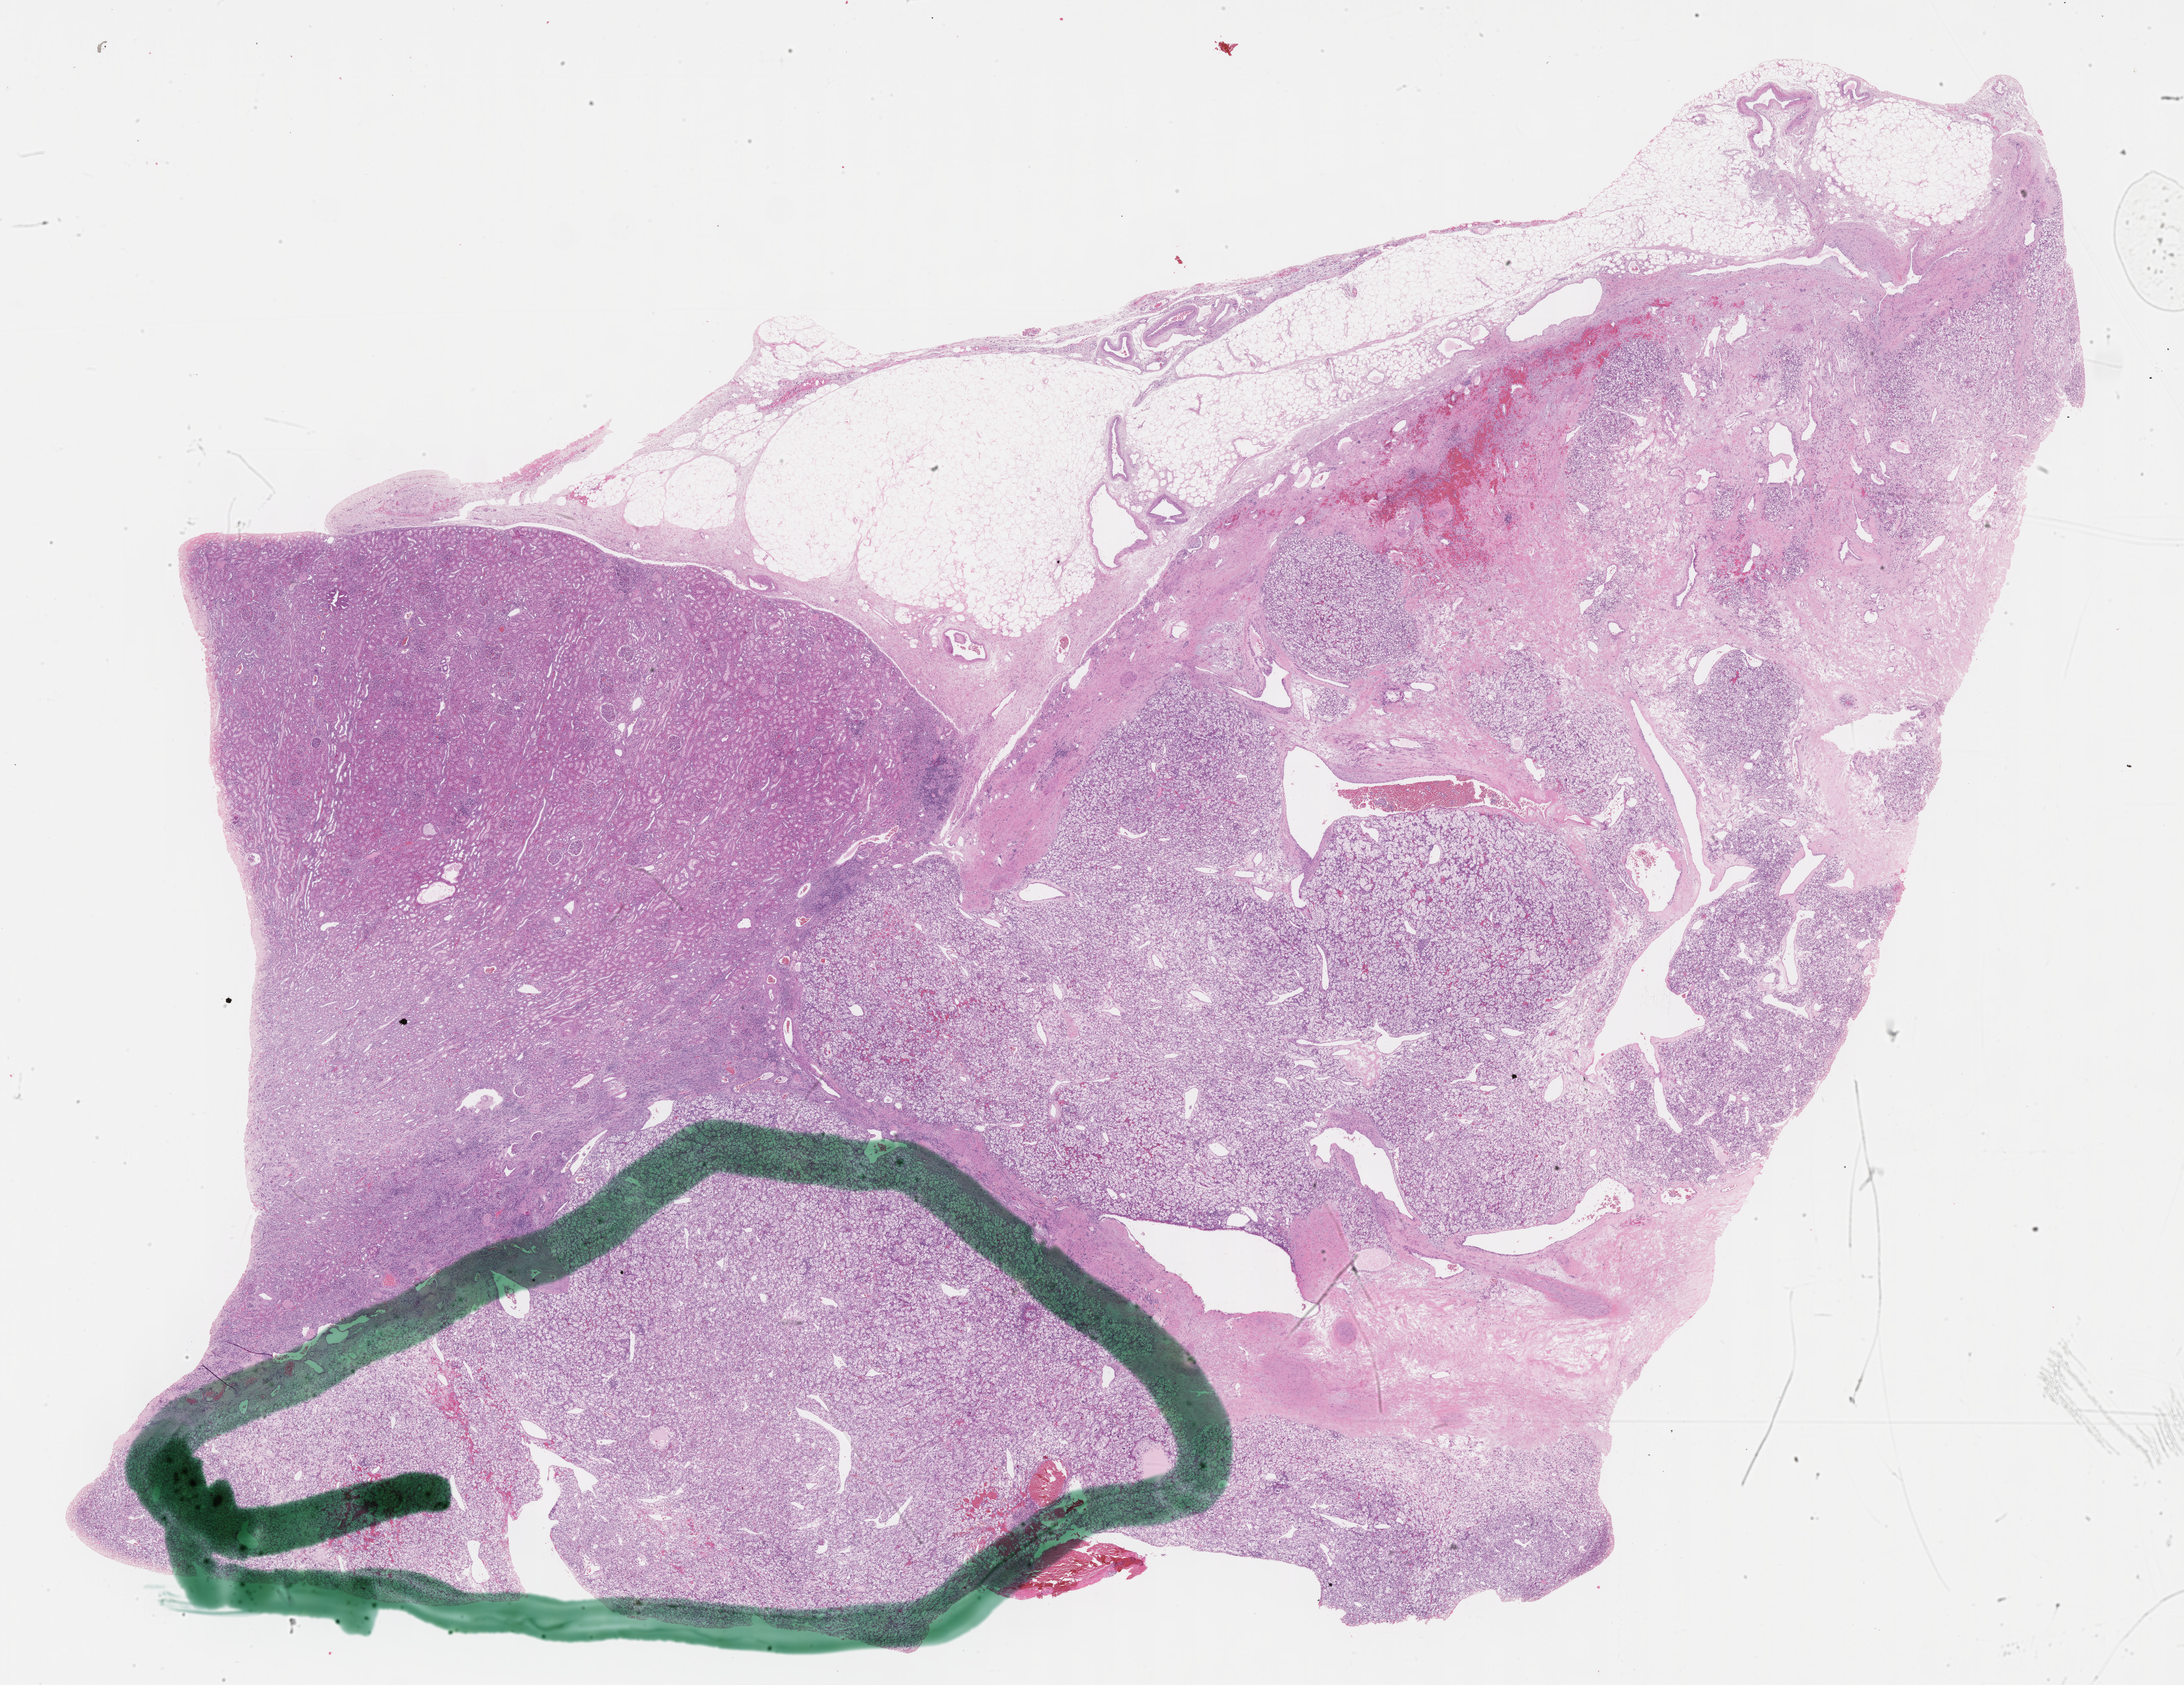
Digitized H&E tissue section (whole slide) — whole scanned area (about 26.7 x 20.6 mm, from a 40x scan) shown as a low-resolution overview, formalin-fixed paraffin-embedded (FFPE) diagnostic section, primary tumour sample from the kidney. Female patient; age at initial diagnosis 73 years. Histologic grade: G3 (poorly differentiated).
AJCC pathologic stage: I. Histologic diagnosis: Clear cell adenocarcinoma, NOS.